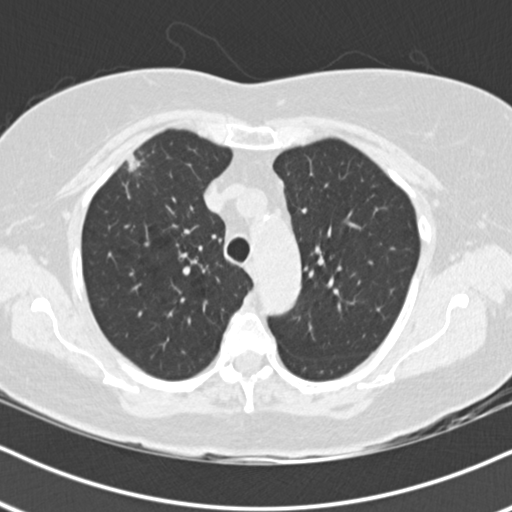
Low-dose screening chest CT, one axial slice. Position 136 of 178 along the scan axis. Lung window (W 1500 / L -600 HU). 2 mm slice thickness. 512 × 512 image matrix, field of view 320 × 320 mm.
Structures marked on this image (manually delineated by an expert):
- lesion 1 (tumor, upper lobe of right lung): bounding box <125,154,141,172> (left, top, right, bottom; pixels)